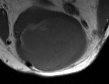
MRI of an extremity soft-tissue mass, one axial slice. Position 25 of 50 along the scan axis. MR volume resampled by the dataset authors to the PET/CT grid (not the native acquisition matrix). 109 × 84 image matrix. Male patient. Case-level facts recorded for this patient, not image findings: histological type: synovial sarcoma; site of the primary tumour: left poplietal fossa.
Annotated regions visible in this slice (expert contour drawn on MRI and transferred to this co-registered scan by the dataset authors):
- gross tumour volume (mass): bounding box [x1, y1, x2, y2] px = [16, 14, 88, 72]